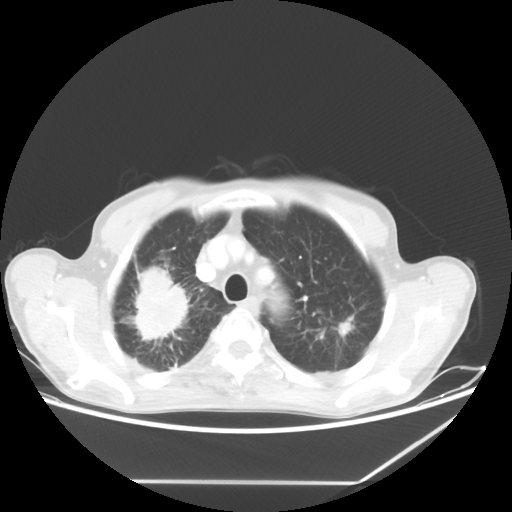
Chest CT, one axial slice. Slice 51 of 65 in the series (ordered by position). 80 kVp. Lung window (W 1500 / L -600 HU). 5 mm slice thickness. 512 × 512 image matrix, field of view 397 × 397 mm. Male patient, age 68 years. Case-level facts recorded for this patient, not image findings: clinical TNM (as recorded): T3 N3 M0.
Annotated regions visible in this slice (bounding box drawn by a radiologist):
- lung tumour (recorded histology: adenocarcinoma): box from (x=126, y=256) to (x=216, y=376) px